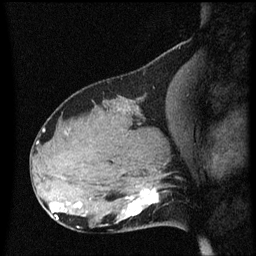
Breast MRI (dynamic contrast-enhanced), one sagittal slice; position 25 of 60 along the scan axis; dynamic contrast-enhanced series, image 2 of 3 at this slice position (ordered by acquisition); 1.5 T; TE 4.2 ms, TR 8.4 ms; 2 mm slice thickness; 256 × 256 image matrix, field of view 200 × 200 mm. Female patient, age 31 years. From the clinical record (not read from this slice): setting: breast cancer imaged before/during neoadjuvant chemotherapy; receptor status: HR-positive, HER2-negative.
Outlined on this slice (semi-automatically segmented with operator editing):
- analysis volume of interest (the breast-tissue region the enhancement analysis was run in; not a lesion): bounding box [x1, y1, x2, y2] px = [102, 166, 176, 229]
- tumour enhancement mask (voxels above the 70 % enhancement threshold inside the analysis volume of interest): [129, 190, 159, 217]